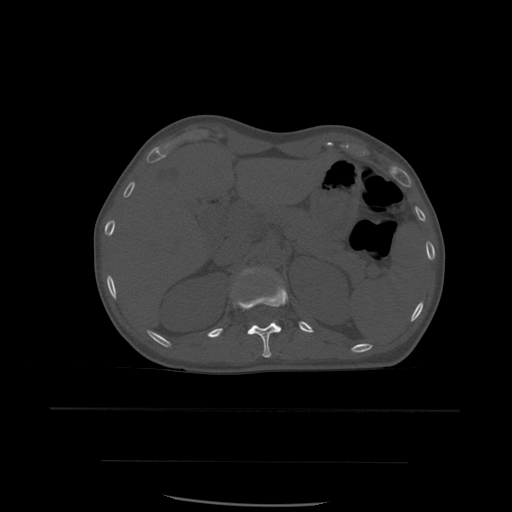
CT including the spine, one axial slice. Position 268 of 574 along the scan axis. Bone window (W 1800 / L 400 HU). 512 × 512 image matrix, field of view 392 × 392 mm. Patient age 48 years. Case-level facts recorded for this patient, not image findings: primary cancer: lung.
Outlined on this slice (semi-automatic segmentation, software-assisted and operator-edited):
- L1 vertebra: bounding box <253,269,258,272> (left, top, right, bottom; pixels)
- T12 vertebra: <233,283,289,358>